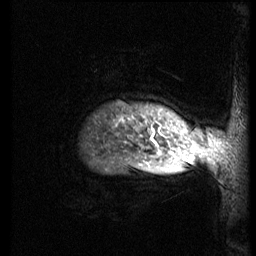
Breast MRI (dynamic contrast-enhanced), one sagittal slice; slice 69 of 74 in the series (ordered by position); 3 images stored at this slice position (order not interpretable as contrast timing); 1.5 T; TE 4.2 ms, TR 8.9 ms; 2.5 mm slice thickness; 256 × 256 image matrix. Patient: female, 57 years. From the clinical record (not read from this slice): setting: breast cancer imaged before/during neoadjuvant chemotherapy; receptor status: HER2-positive.
Outlined on this slice (semi-automatic segmentation, software-assisted and operator-edited):
- analysis volume of interest (the breast-tissue region the enhancement analysis was run in; not a lesion): box from (x=82, y=77) to (x=248, y=173) px
- tumour enhancement mask (voxels above the 140 % enhancement threshold inside the analysis volume of interest): (x=152, y=124)–(x=162, y=156)